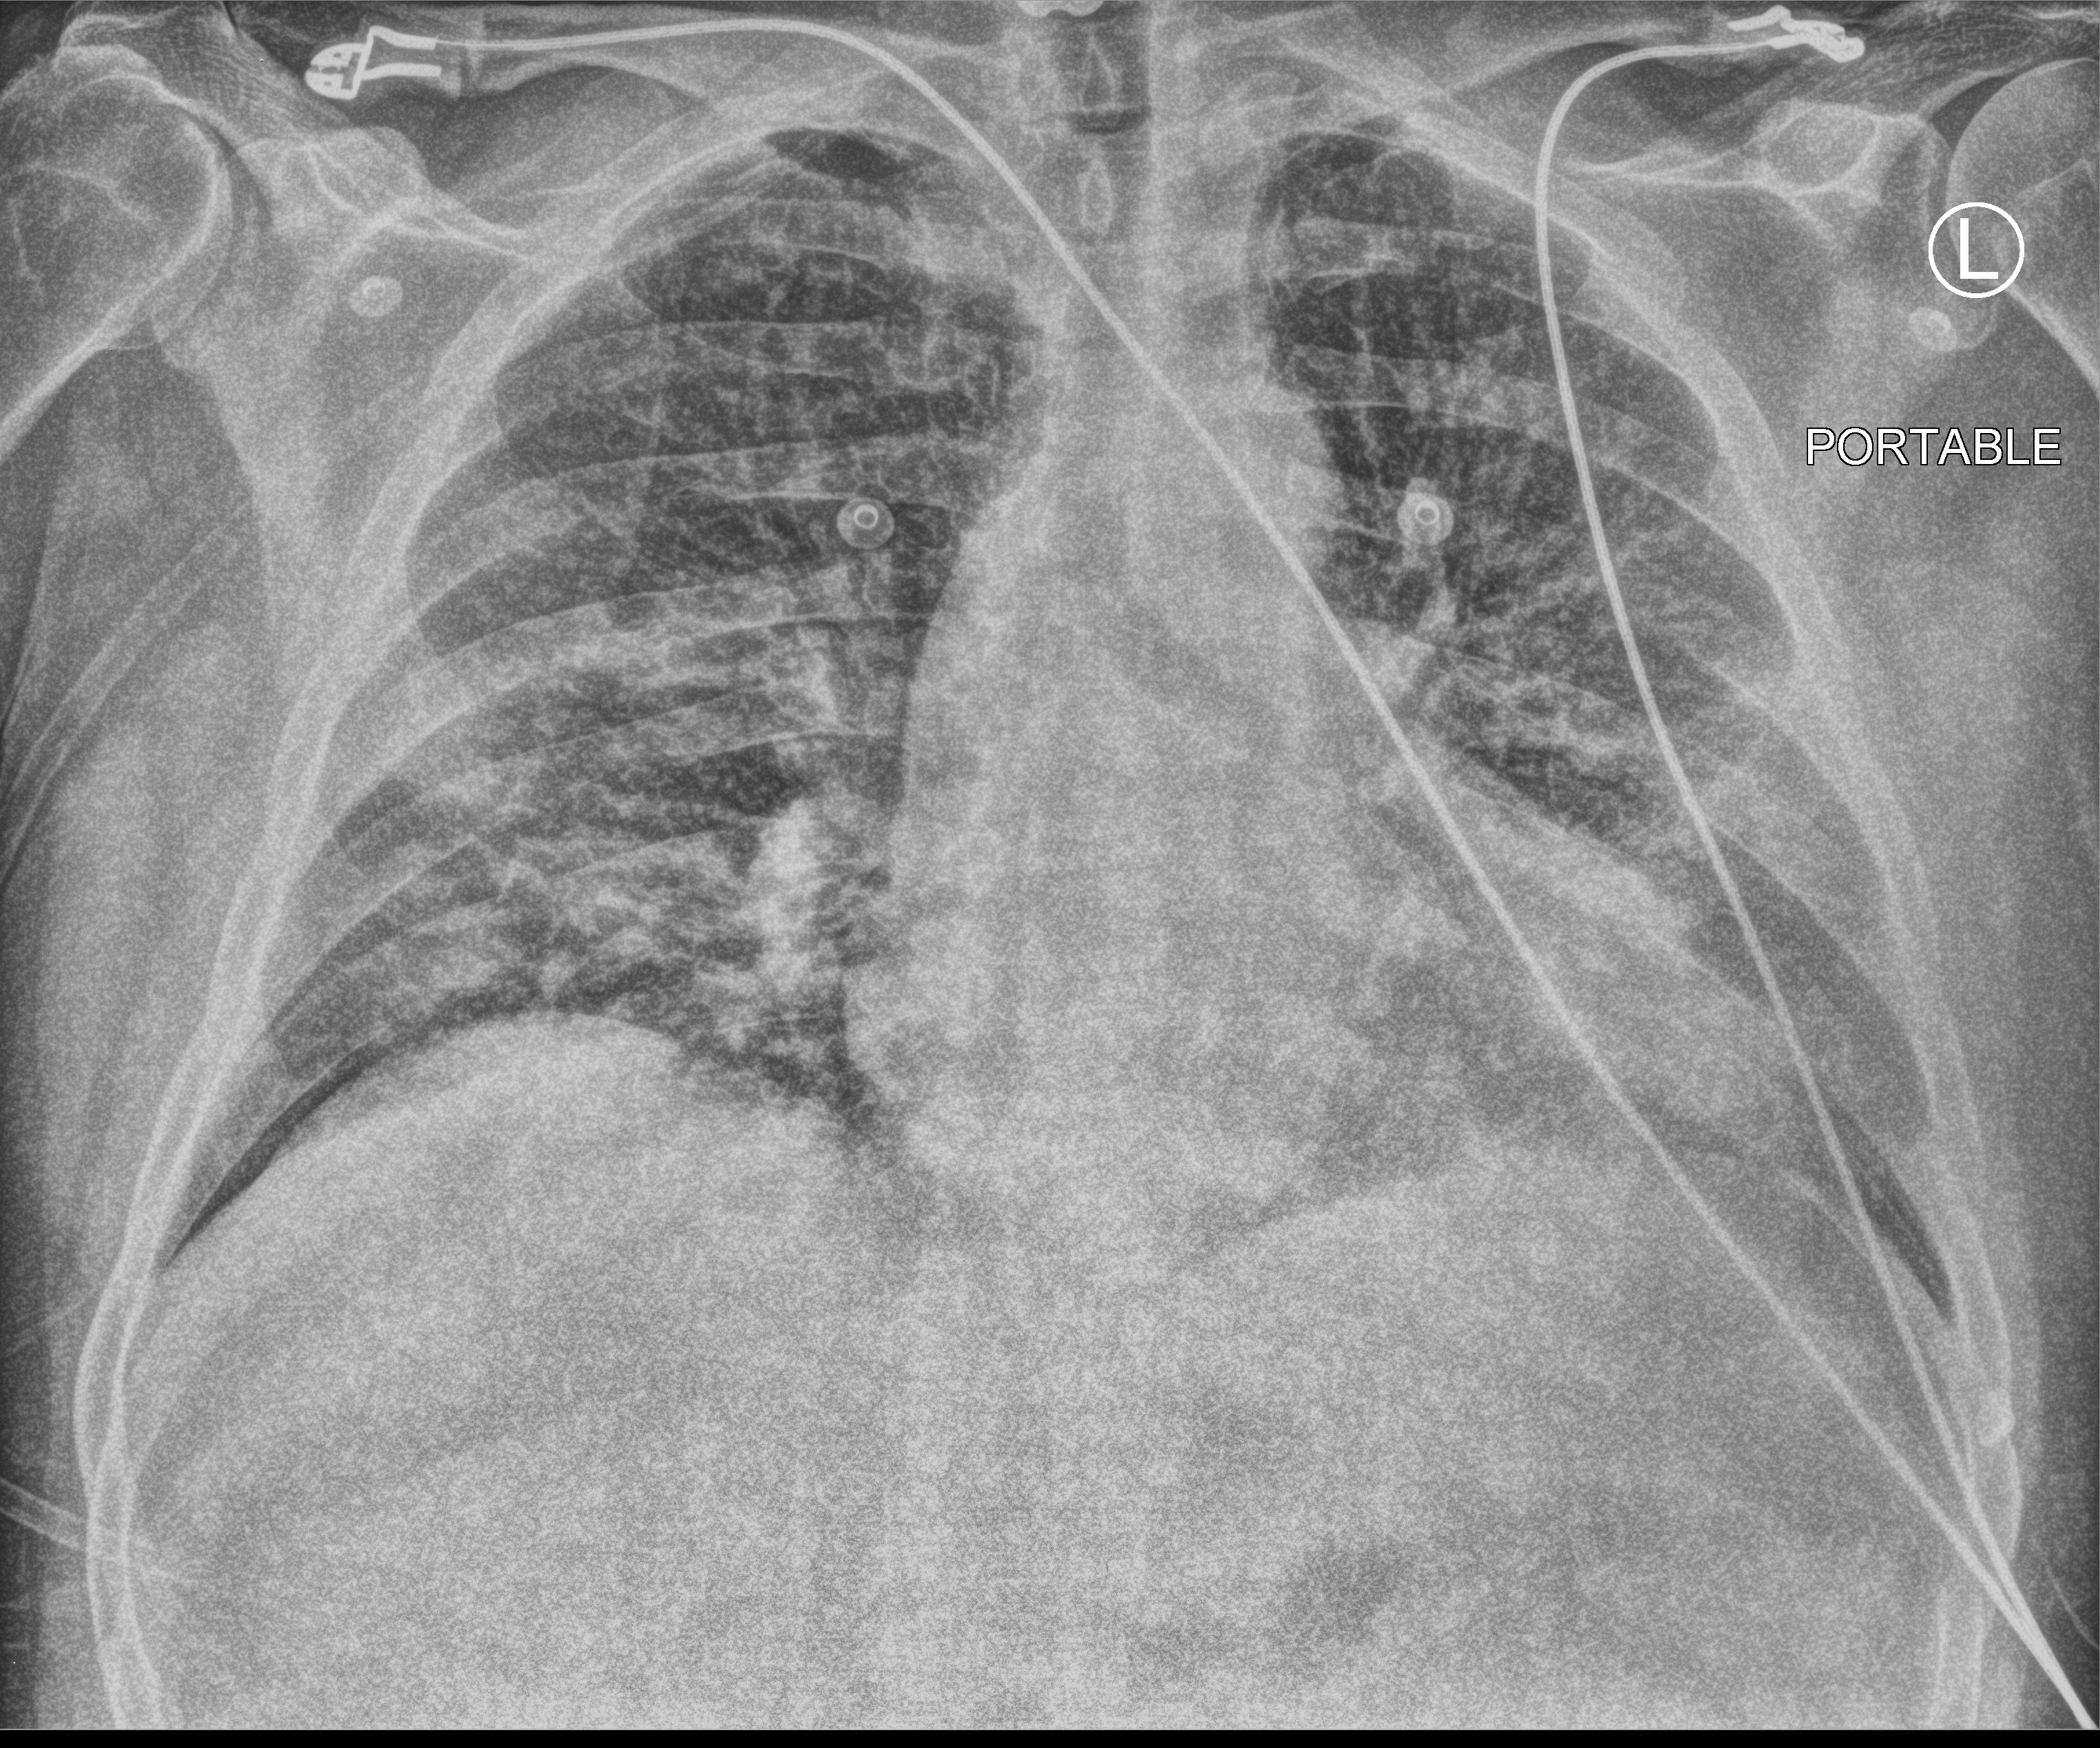
Portable chest radiograph; anteroposterior (AP) projection. Patient hospitalised with COVID-19; male, aged 60–74 years.
Admission-level facts for this patient (not findings on this image; timing relative to this image not recorded):
- mechanically ventilated during this hospital stay: no
- admitted to intensive care during this hospital stay: no